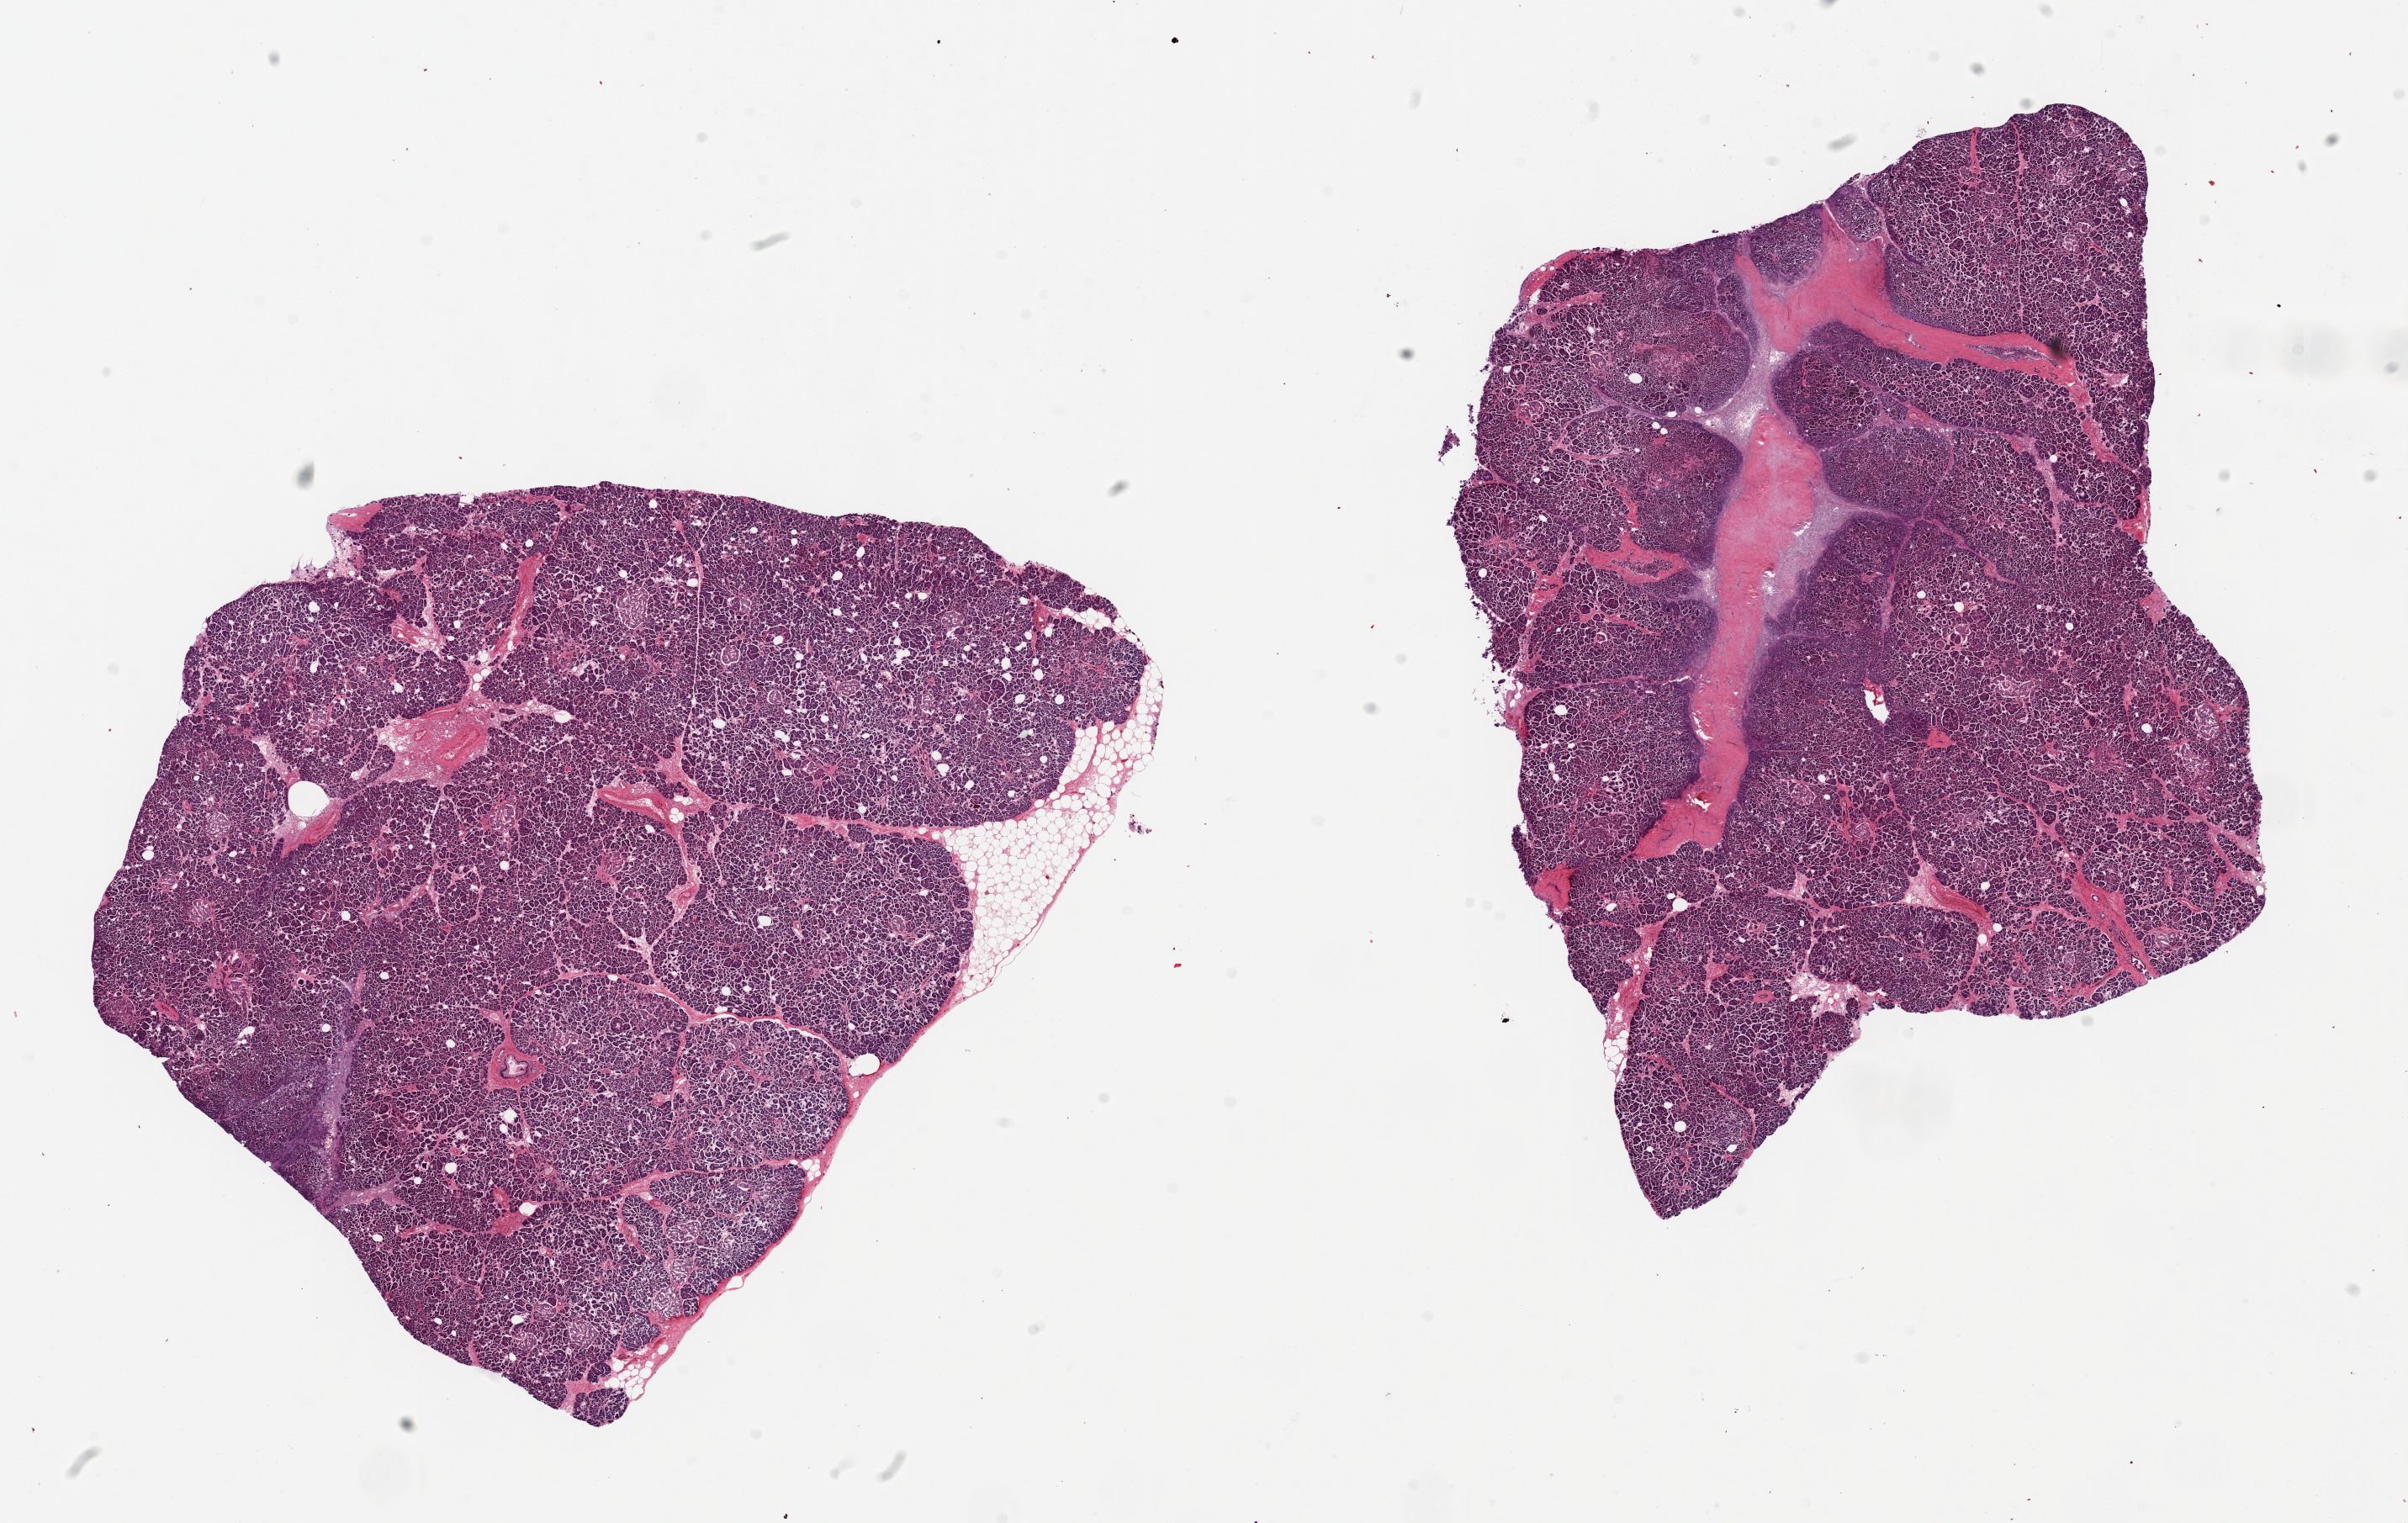
Haematoxylin and eosin whole-slide image — shown as a low-resolution overview of the whole scanned area (about 22.6 x 14.3 mm, acquisition: 20x scan), PAXgene-fixed, paraffin-embedded tissue, sampled site (target tissue): pancreas, donor tissue sample. Donor sex: female.
Reviewer comment on this tissue sample: 2 pieces ~9x7mm, moderate autolysis/saponification; Islets reasonably well-visualized; Minimal adherent fat.